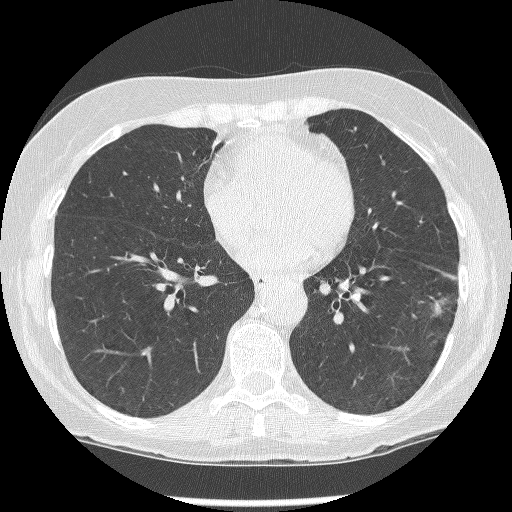
Low-dose screening chest CT, axial slice, baseline annual screen, lung window (W 1500 / L -600 HU), 1.25 mm slice thickness, lung (sharp) reconstruction kernel (BONE), slice 101 of 247 in the series, 512 × 512 image matrix, field of view 303 × 303 mm. Female participant, aged 62 years at enrolment. Former smoker at enrolment.
• Lesion marked by an expert reader, bounding box [x1, y1, x2, y2] px = [413, 283, 460, 346].
• The screening reader recorded 2 non-calcified nodules or masses ≥4 mm on this exam (left lower lobe, left lower lobe); which of them this box marks is not recorded.
• Official screen result: positive, change unspecified: nodule(s) >= 4 mm or enlarging nodule(s), mass(es), or other non-specific abnormalities suspicious for lung cancer.
• Later outcome: lung cancer diagnosed 15 days after this screen — non-small cell carcinoma, left lower lobe, stage IIIB (AJCC 6th edition), 23 mm at pathology.